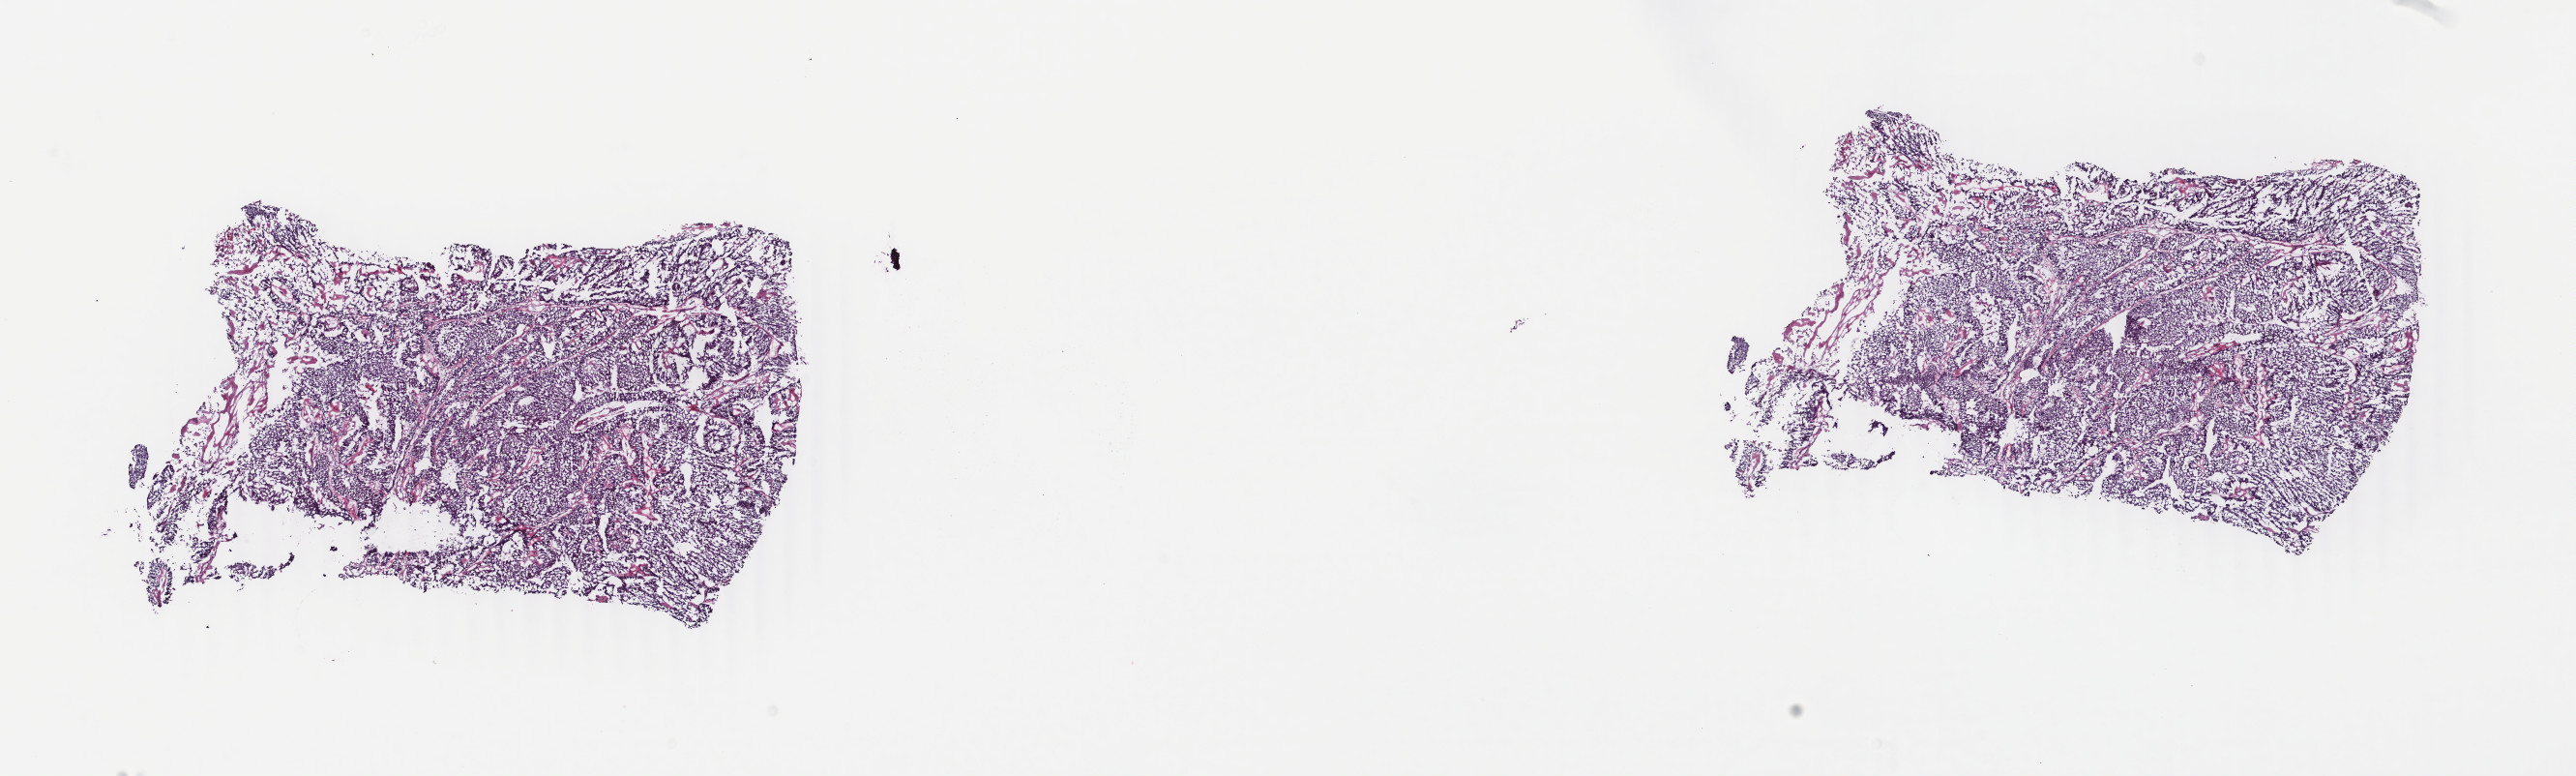
H&E-stained whole-slide image — whole scanned area (about 21.2 x 6.4 mm, acquisition: 40x scan) shown as a low-resolution overview. Frozen section from the top of the tissue portion. Primary tumour sample from the bladder. Patient: male, age at initial diagnosis 65 years. Histologic grade: high grade. Composition of this section per pathologist review: tumour cells 90%, tumour nuclei 90%, normal cells 0%, stromal cells 10%, necrosis 0%. Infiltration values recorded for this section: lymphocyte infiltration 1%, monocyte infiltration 1%, neutrophil infiltration 1%.
* AJCC pathologic stage: III (6th edition)
* diagnosis: Transitional cell carcinoma
* lymph nodes positive (case pathology): 0 of 46 examined
* TNM: T3 N0 M0